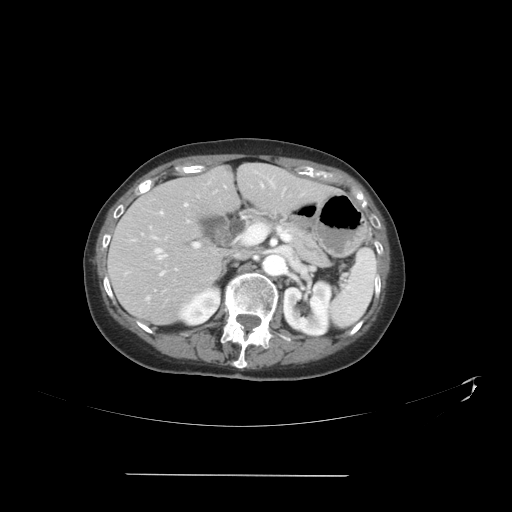
Contrast-enhanced abdominal CT, one axial slice. Position 22 of 41 along the scan axis. Reconstruction kernel STANDARD. 120 kVp. Intravenous contrast given. Soft-tissue window (W 400 / L 40 HU). 5 mm slice thickness. 512 × 512 image matrix, field of view 431 × 431 mm. Female patient, age 74 years. Case-level facts recorded for this patient, not image findings: diagnosis: colorectal cancer liver metastases, imaged before liver resection; multiple liver metastases: yes; largest metastasis: 3.3 cm; disease in both lobes: yes.
Structures marked on this image (expert manual segmentation):
- hepatic veins: box from (x=146, y=191) to (x=217, y=300) px
- liver: (x=110, y=165)–(x=333, y=324)
- planned liver remnant (the part of the liver to remain after resection): (x=117, y=165)–(x=322, y=245)
- portal vein (with intrahepatic branches): (x=150, y=182)–(x=272, y=275)